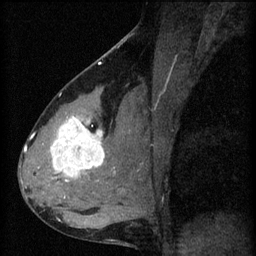
Breast MRI (dynamic contrast-enhanced), one sagittal slice. Position 35 of 60 along the scan axis. 3 images stored at this slice position (order not interpretable as contrast timing). 1.5 T. TE 4.2 ms, TR 8.2 ms. 2 mm slice thickness. 256 × 256 image matrix. Patient: female, 37 years.
Annotated regions visible in this slice (semi-automatically segmented with operator editing):
- analysis volume of interest (the breast-tissue region the enhancement analysis was run in; not a lesion): bounding box [x1, y1, x2, y2] px = [44, 100, 119, 197]
- tumour enhancement mask (voxels above the 70 % enhancement threshold inside the analysis volume of interest): [51, 116, 106, 179]